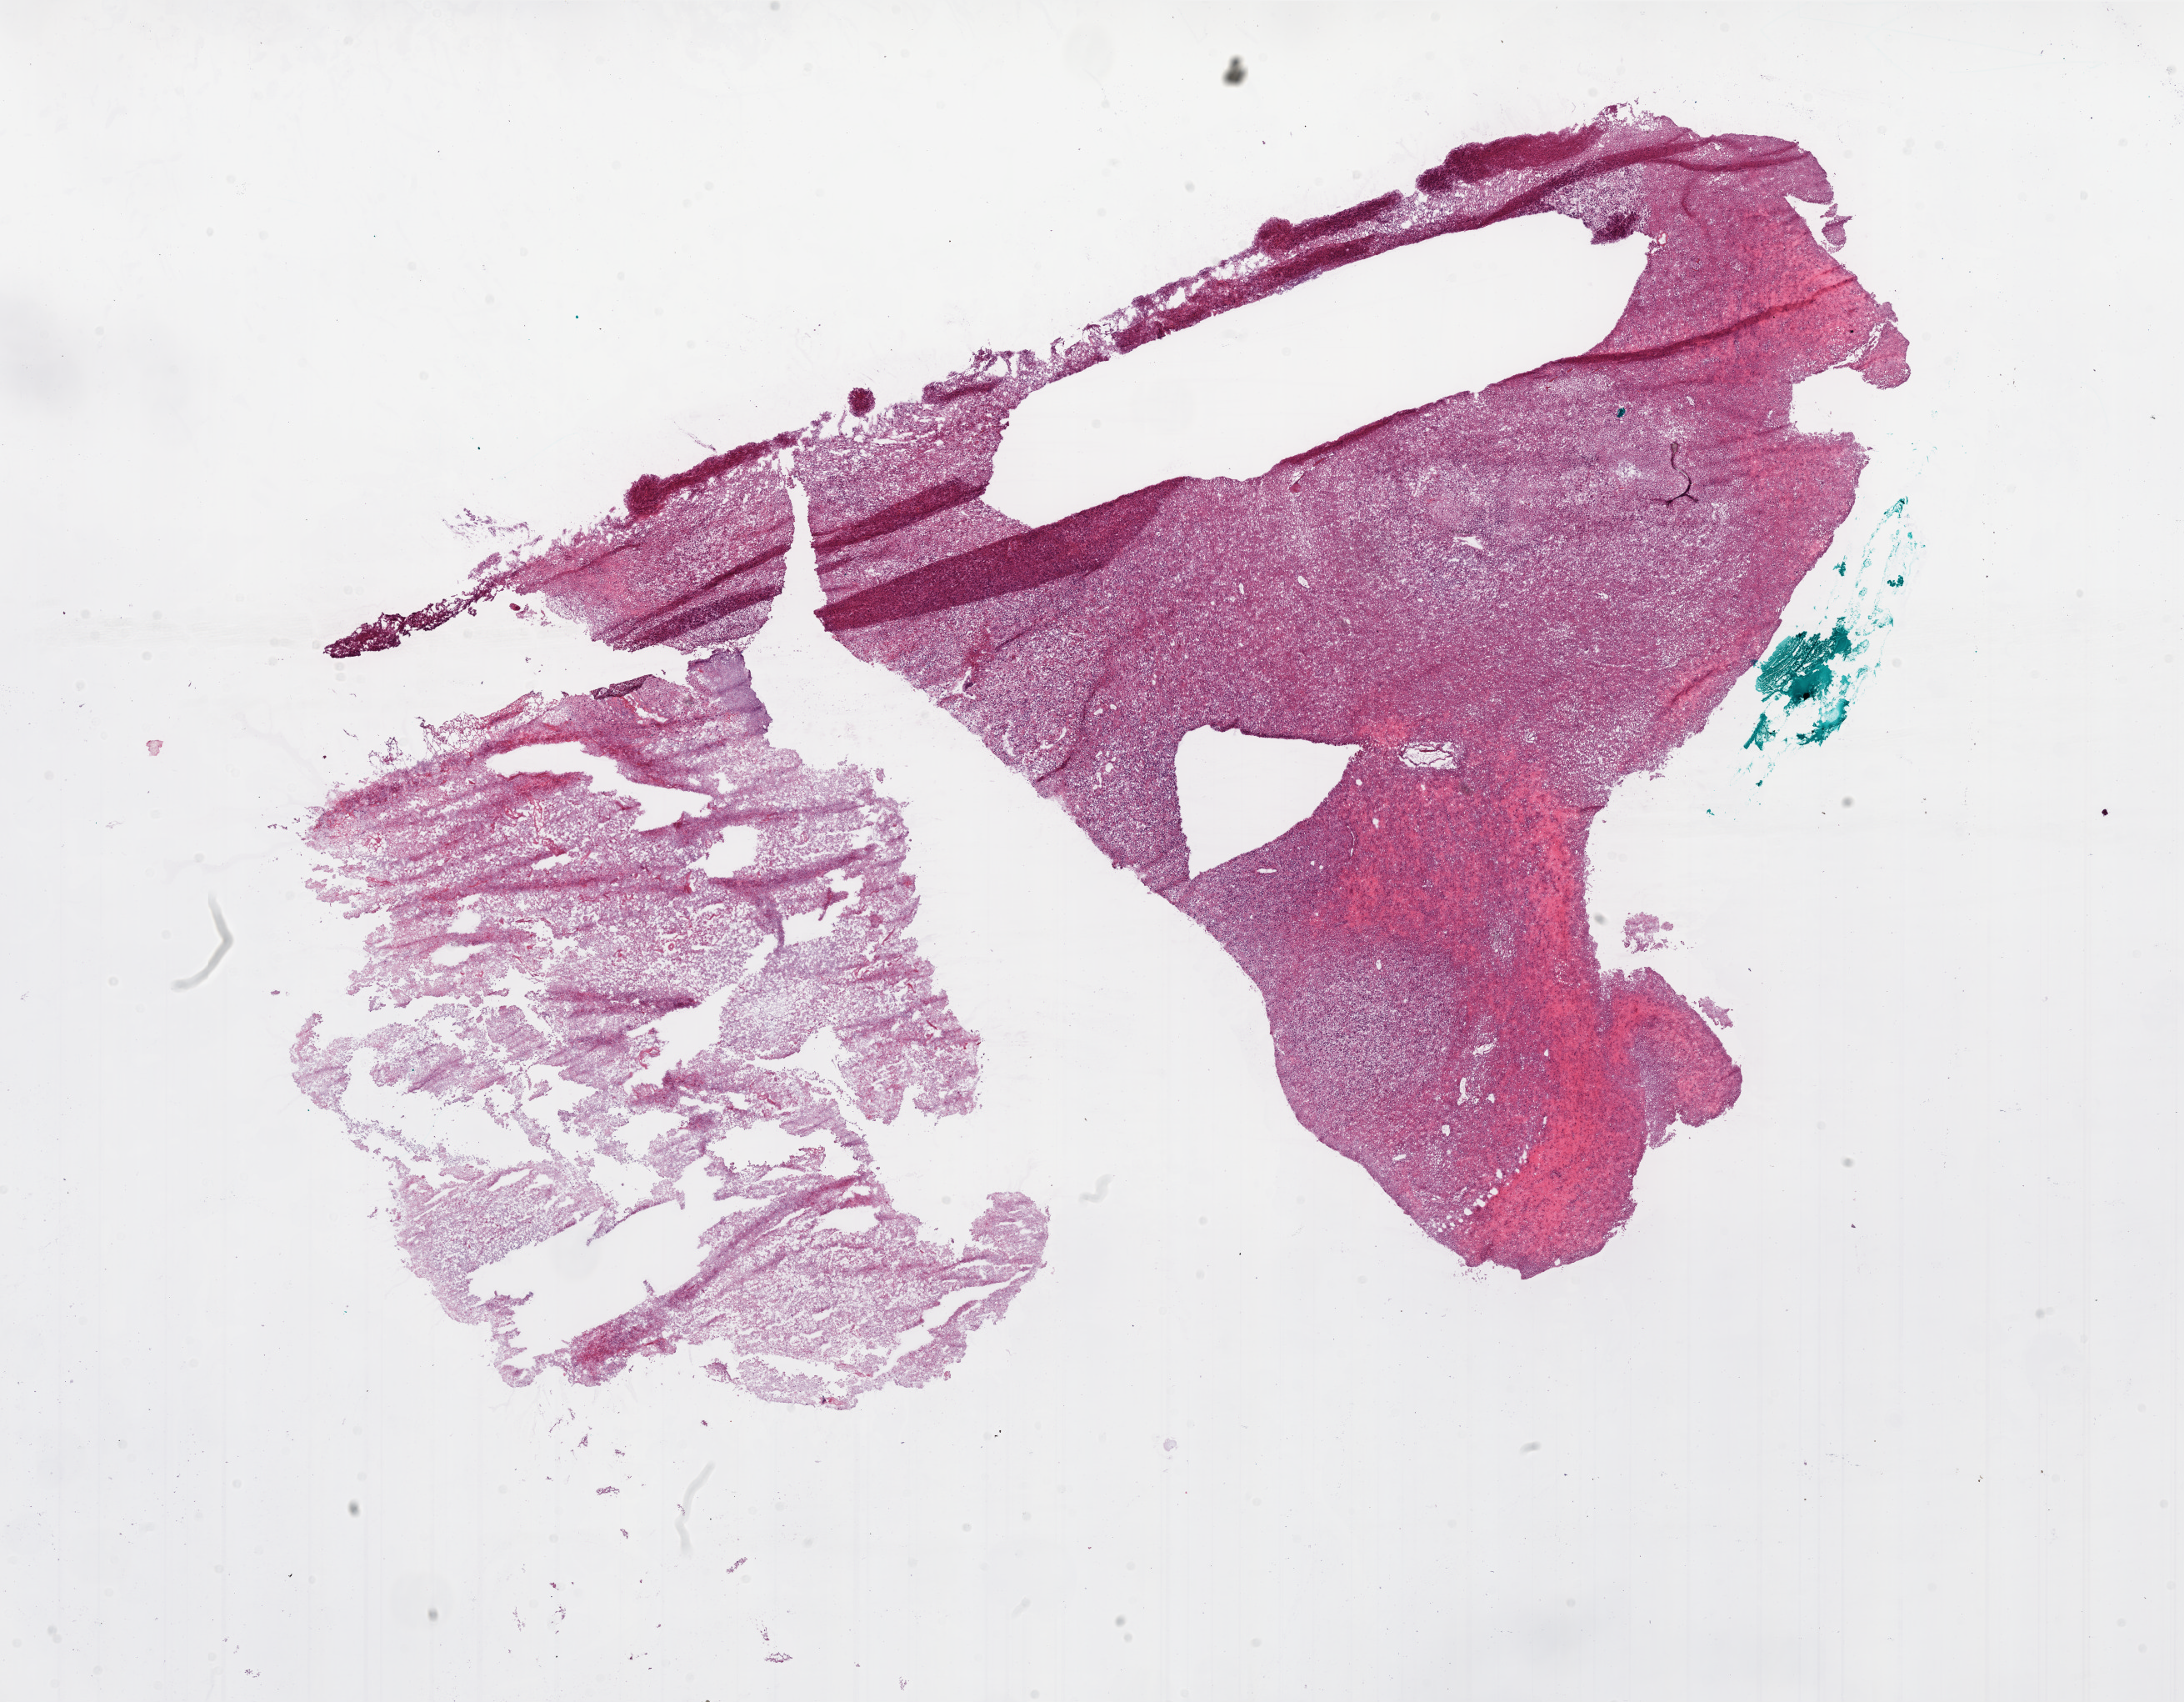
Digitized H&E tissue section (whole slide) — a low-resolution overview of the entire scanned area, about 21.0 x 16.3 mm, frozen section from the bottom of the tissue portion, sample: primary tumour, brain. Female patient; age at initial diagnosis 70 years. Composition of this section per pathologist review: tumour cells 50%, tumour nuclei 90%, normal cells 0%, stromal cells 10%, necrosis 40%. Inflammatory infiltration, as recorded: lymphocyte infiltration 0%.
• diagnosis: Glioblastoma